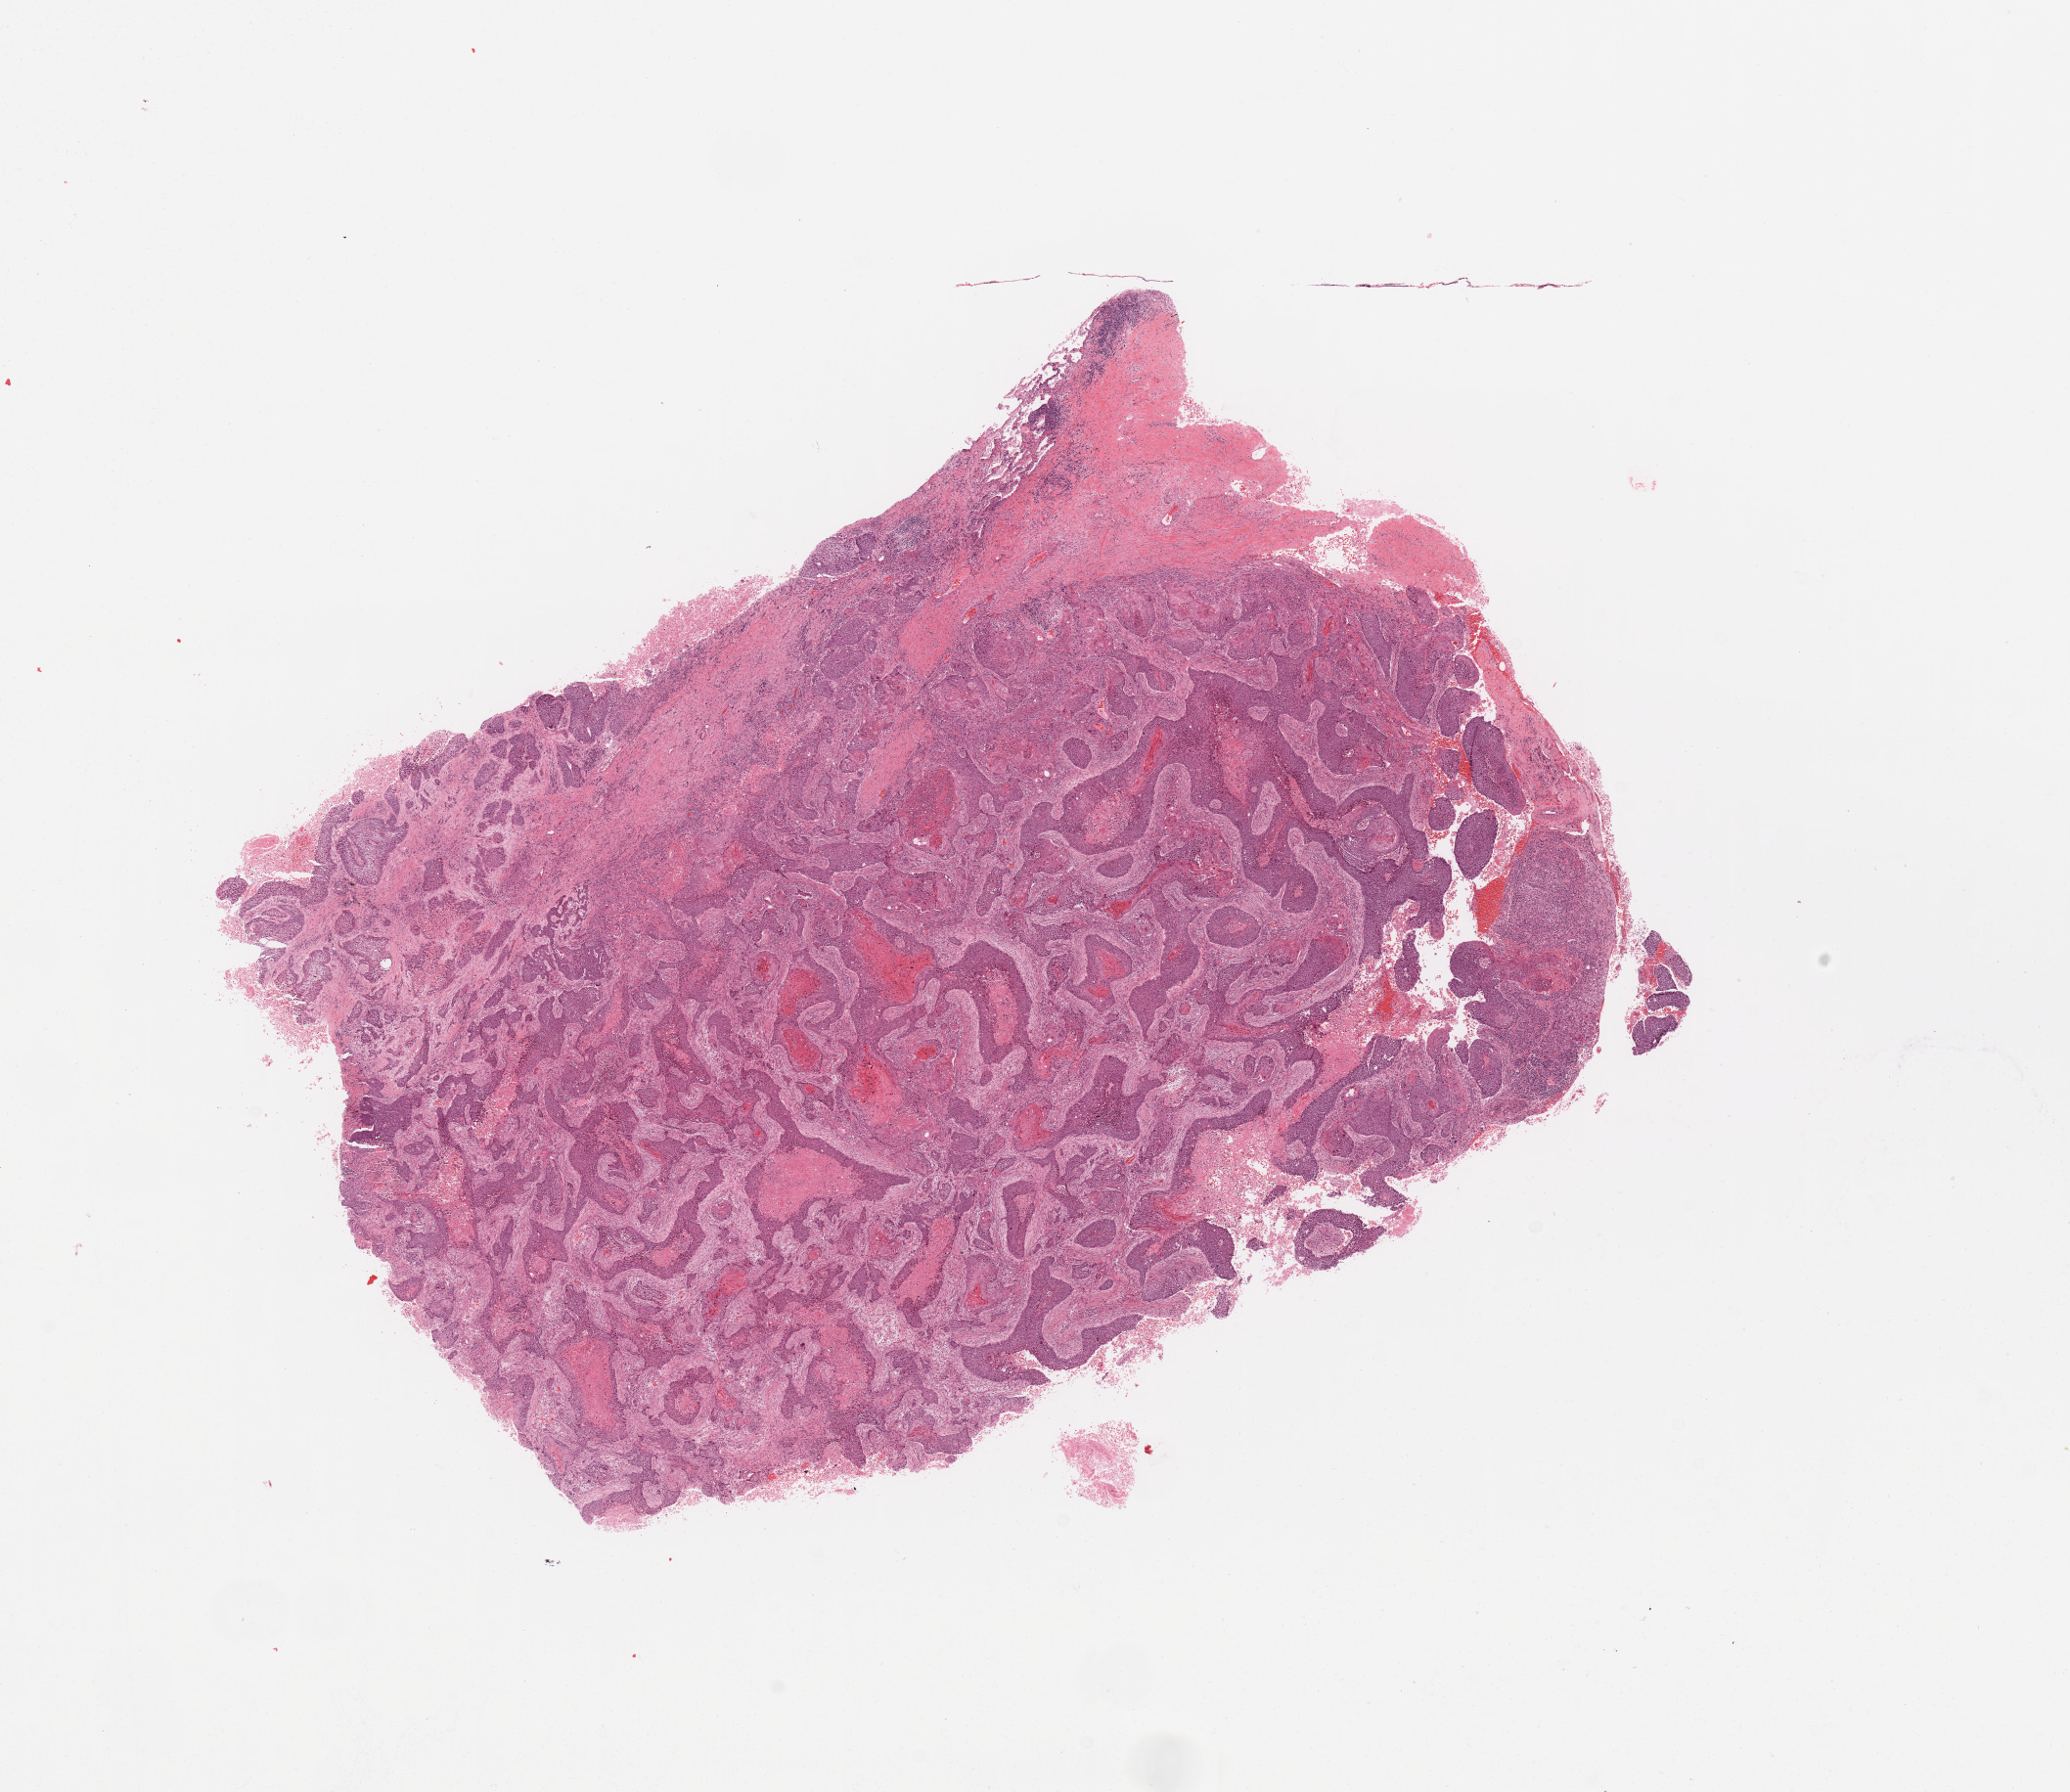
Digitized H&E-stained tissue section (whole slide) — whole scanned area (about 16.7 x 14.5 mm, slide scanned at 20x) shown as a low-resolution overview, tumour tissue sample, sampled site: lung. Male, 69 y/o. Histologic grade: G2 (moderately differentiated). Pathologist review of this section (percent, as recorded): tumour nuclei 70%, necrosis 5%.
* primary tumour site (as recorded): left lower lobe
* AJCC pathologic stage: IA
* diagnosis: Squamous cell carcinoma, NOS